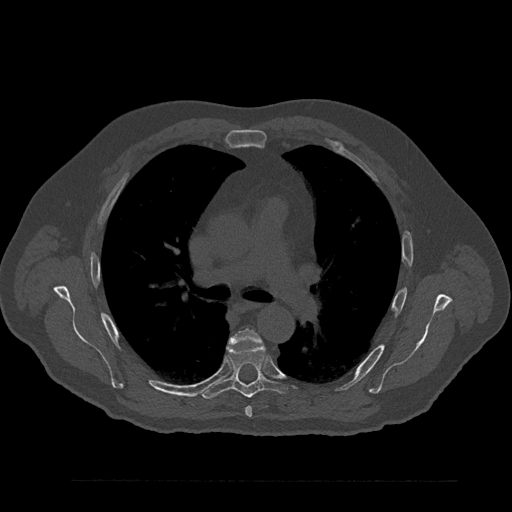
CT including the spine, one axial slice. Position 567 of 797 along the scan axis. Reconstruction kernel Br40s/3. 120 kVp. Bone window (W 1800 / L 400 HU). 0.5 mm slice thickness. 512 × 512 image matrix. Patient: male, 61 years. From the clinical record (not read from this slice): primary cancer: prostate.
Outlined on this slice (semi-automatic segmentation, software-assisted and operator-edited):
- T5 vertebra: bounding box <230,328,262,418> (left, top, right, bottom; pixels)
- T6 vertebra: <202,344,287,399>